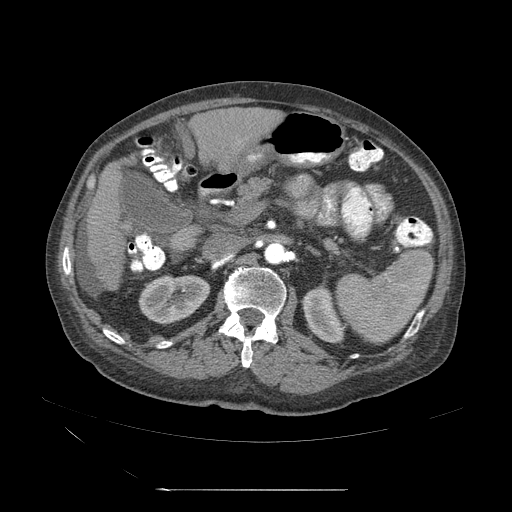
Contrast-enhanced abdominal CT (liver protocol), one axial slice. Position 18 of 71 along the scan axis. Reconstruction kernel STANDARD. Soft-tissue window (W 400 / L 40 HU). 2.5 mm slice thickness. 512 × 512 image matrix, field of view 440 × 440 mm. Case-level facts recorded for this patient, not image findings: diagnosis: hepatocellular carcinoma (patient treated with transarterial chemoembolisation; whether this scan precedes or follows treatment is not stated here); TNM stage (as recorded): Stage-II; Child-Pugh class: A; tumour nodularity: multinodular; tumour size: 1 cm.
Annotated regions visible in this slice (semi-automatic segmentation, software-assisted and operator-edited):
- abdominal aorta: bounding box <264,243,286,267> (left, top, right, bottom; pixels)
- liver parenchyma outside the tumour (the mass and vessels are separate outlines, so this box may not span the whole liver): <88,172,135,293>